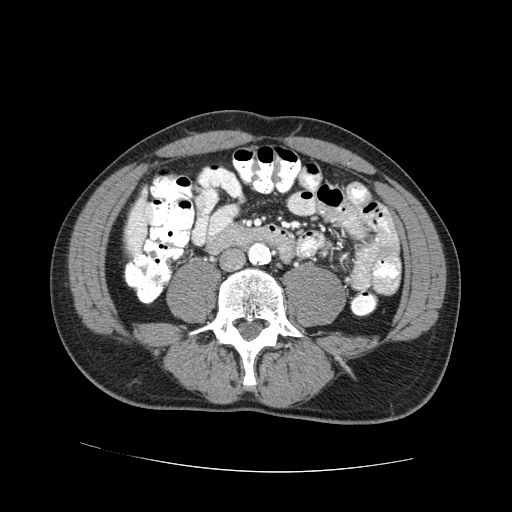
Contrast-enhanced abdominal CT (liver protocol), one axial slice; position 4 of 73 along the scan axis; reconstruction kernel STANDARD; one of 2 acquisitions stored at this slice position; soft-tissue window (W 400 / L 40 HU); 2.5 mm slice thickness; 512 × 512 image matrix, field of view 380 × 380 mm. Case-level facts recorded for this patient, not image findings: diagnosis: hepatocellular carcinoma (patient treated with transarterial chemoembolisation; whether this scan precedes or follows treatment is not stated here); TNM stage (as recorded): Stage-IVA; Child-Pugh class: A.
Structures marked on this image (semi-automatic segmentation, software-assisted and operator-edited):
- liver parenchyma outside the tumour (the mass and vessels are separate outlines, so this box may not span the whole liver): box from (x=126, y=198) to (x=148, y=252) px